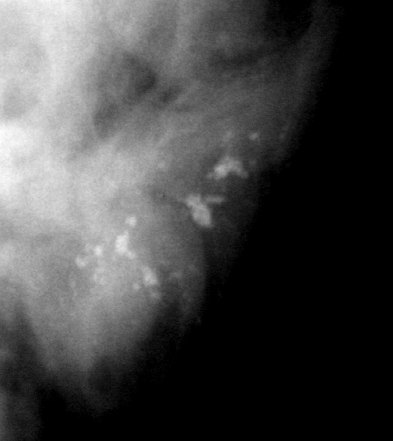
Cropped region of a digitized screen-film mammogram centred on a radiologist-marked abnormality, left breast, MLO view, BI-RADS breast density category 2 (scale 1–4).
- Finding: calcifications, morphology pleomorphic, distribution clustered; BI-RADS assessment category 4; subtlety rating 4 on a 1 (subtle) to 5 (obvious) scale; pathology result (as recorded, not read from the image): malignant.